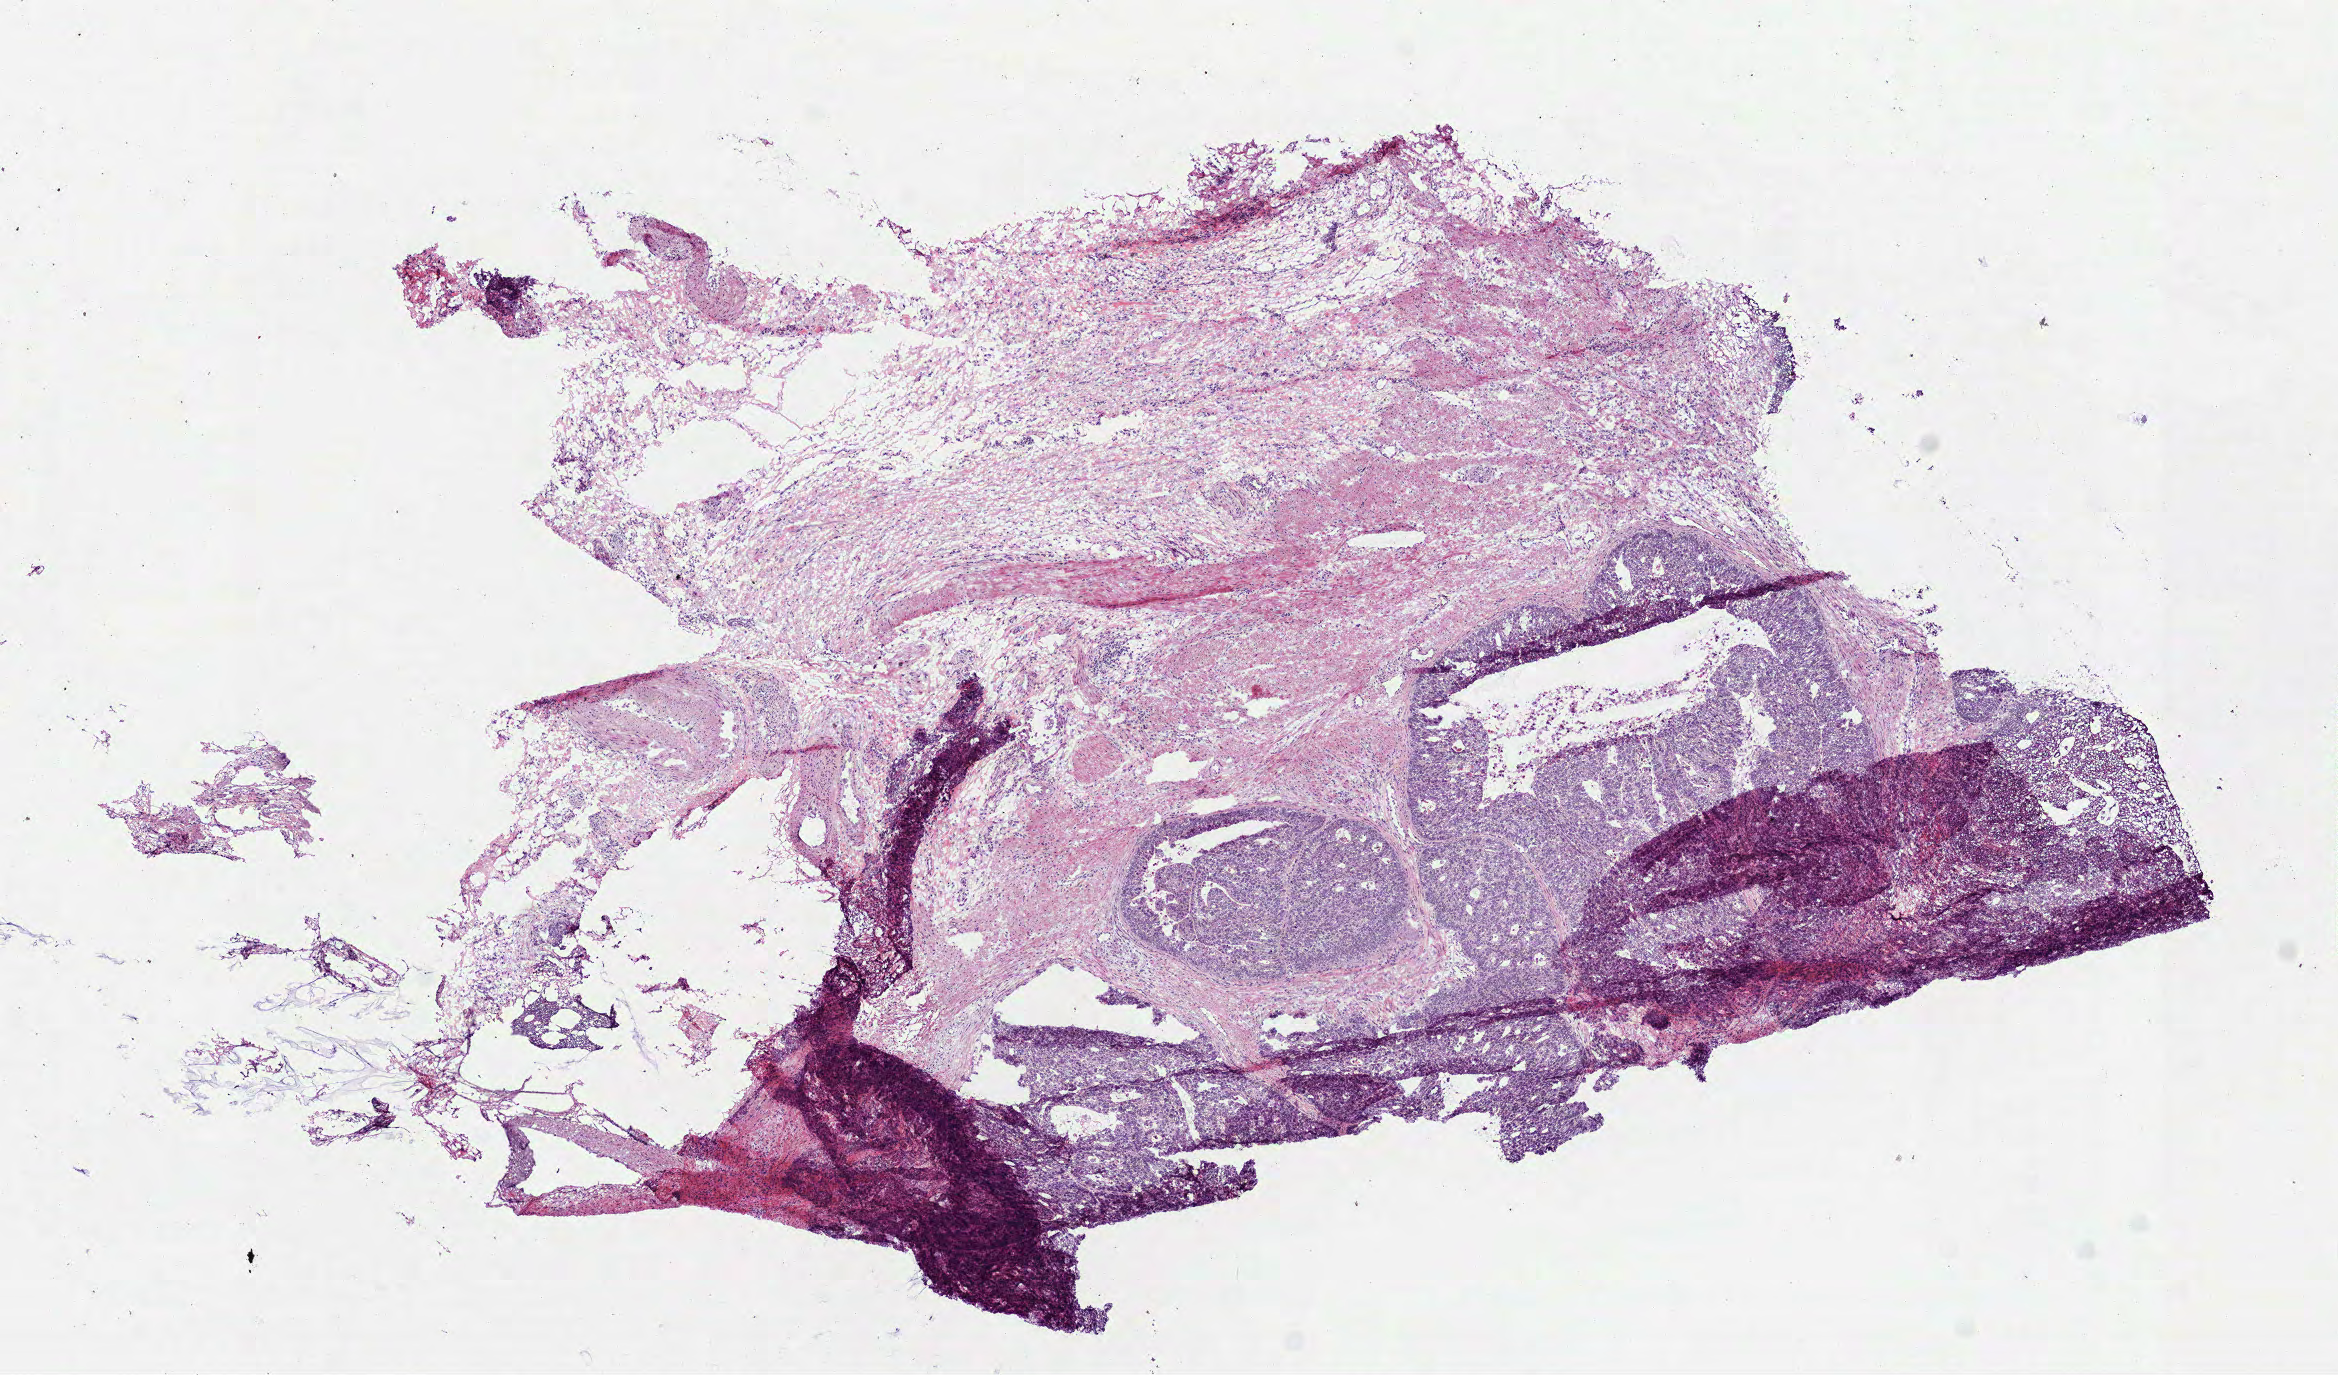
Digitized Hematoxylin and eosin (H&E) stained tissue section (whole slide), shown as a low-resolution overview of the whole scanned area (about 9.4 x 5.5 mm, slide scanned at 40x), frozen section from the bottom of the tissue portion, sample: primary tumour, colon. Female patient; age at initial diagnosis 79 years. Pathologist review of this section (percent, as recorded): tumour cells 50%, tumour nuclei 71%, normal cells 50%, stromal cells 0%, necrosis 0%. Infiltration values recorded for this section: lymphocyte infiltration 10%, monocyte infiltration 1%, neutrophil infiltration 2%.
Pathologic diagnosis: Adenocarcinoma, NOS (hepatic flexure of colon). Lymph nodes positive (case pathology): 10 of 14 examined. AJCC pathologic stage: IIIB.